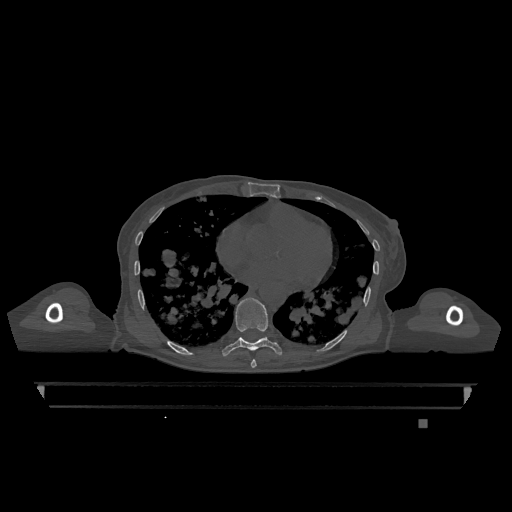
CT including the spine, one axial slice; slice 691 of 1317 in the series (ordered by position); bone window (W 1800 / L 400 HU); 0.5 mm slice thickness; 512 × 512 image matrix, field of view 500 × 500 mm. Female patient, age 74 years. From the clinical record (not read from this slice): primary cancer: lung; vertebrae with lytic lesions (as recorded): T1, T4, T5, T6, L4, L5.
Structures marked on this image (semi-automatic segmentation, software-assisted and operator-edited):
- T7 vertebra: bounding box (x1, y1, x2, y2) in pixels: (251, 359, 257, 368)
- T9 vertebra: (222, 298, 282, 357)